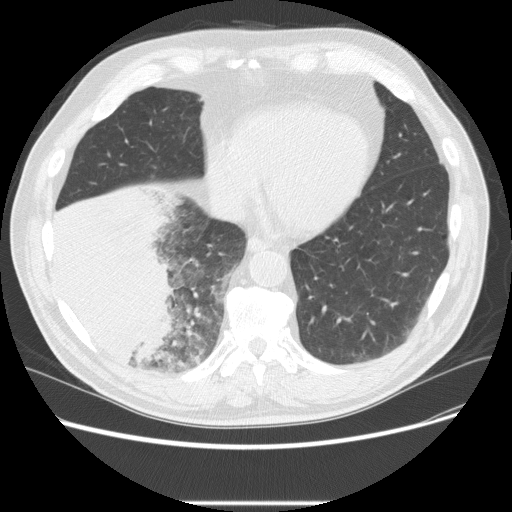
Low-dose screening chest CT, one axial slice. Slice 69 of 233 in the series (ordered by position). Reconstruction kernel STANDARD. Lung window (W 1500 / L -600 HU). 2.5 mm slice thickness. 512 × 512 image matrix.
Outlined on this slice (manually delineated by an expert):
- lesion 3 (tumor, lower lobe of right lung): bounding box (x1, y1, x2, y2) in pixels: (51, 198, 177, 367)